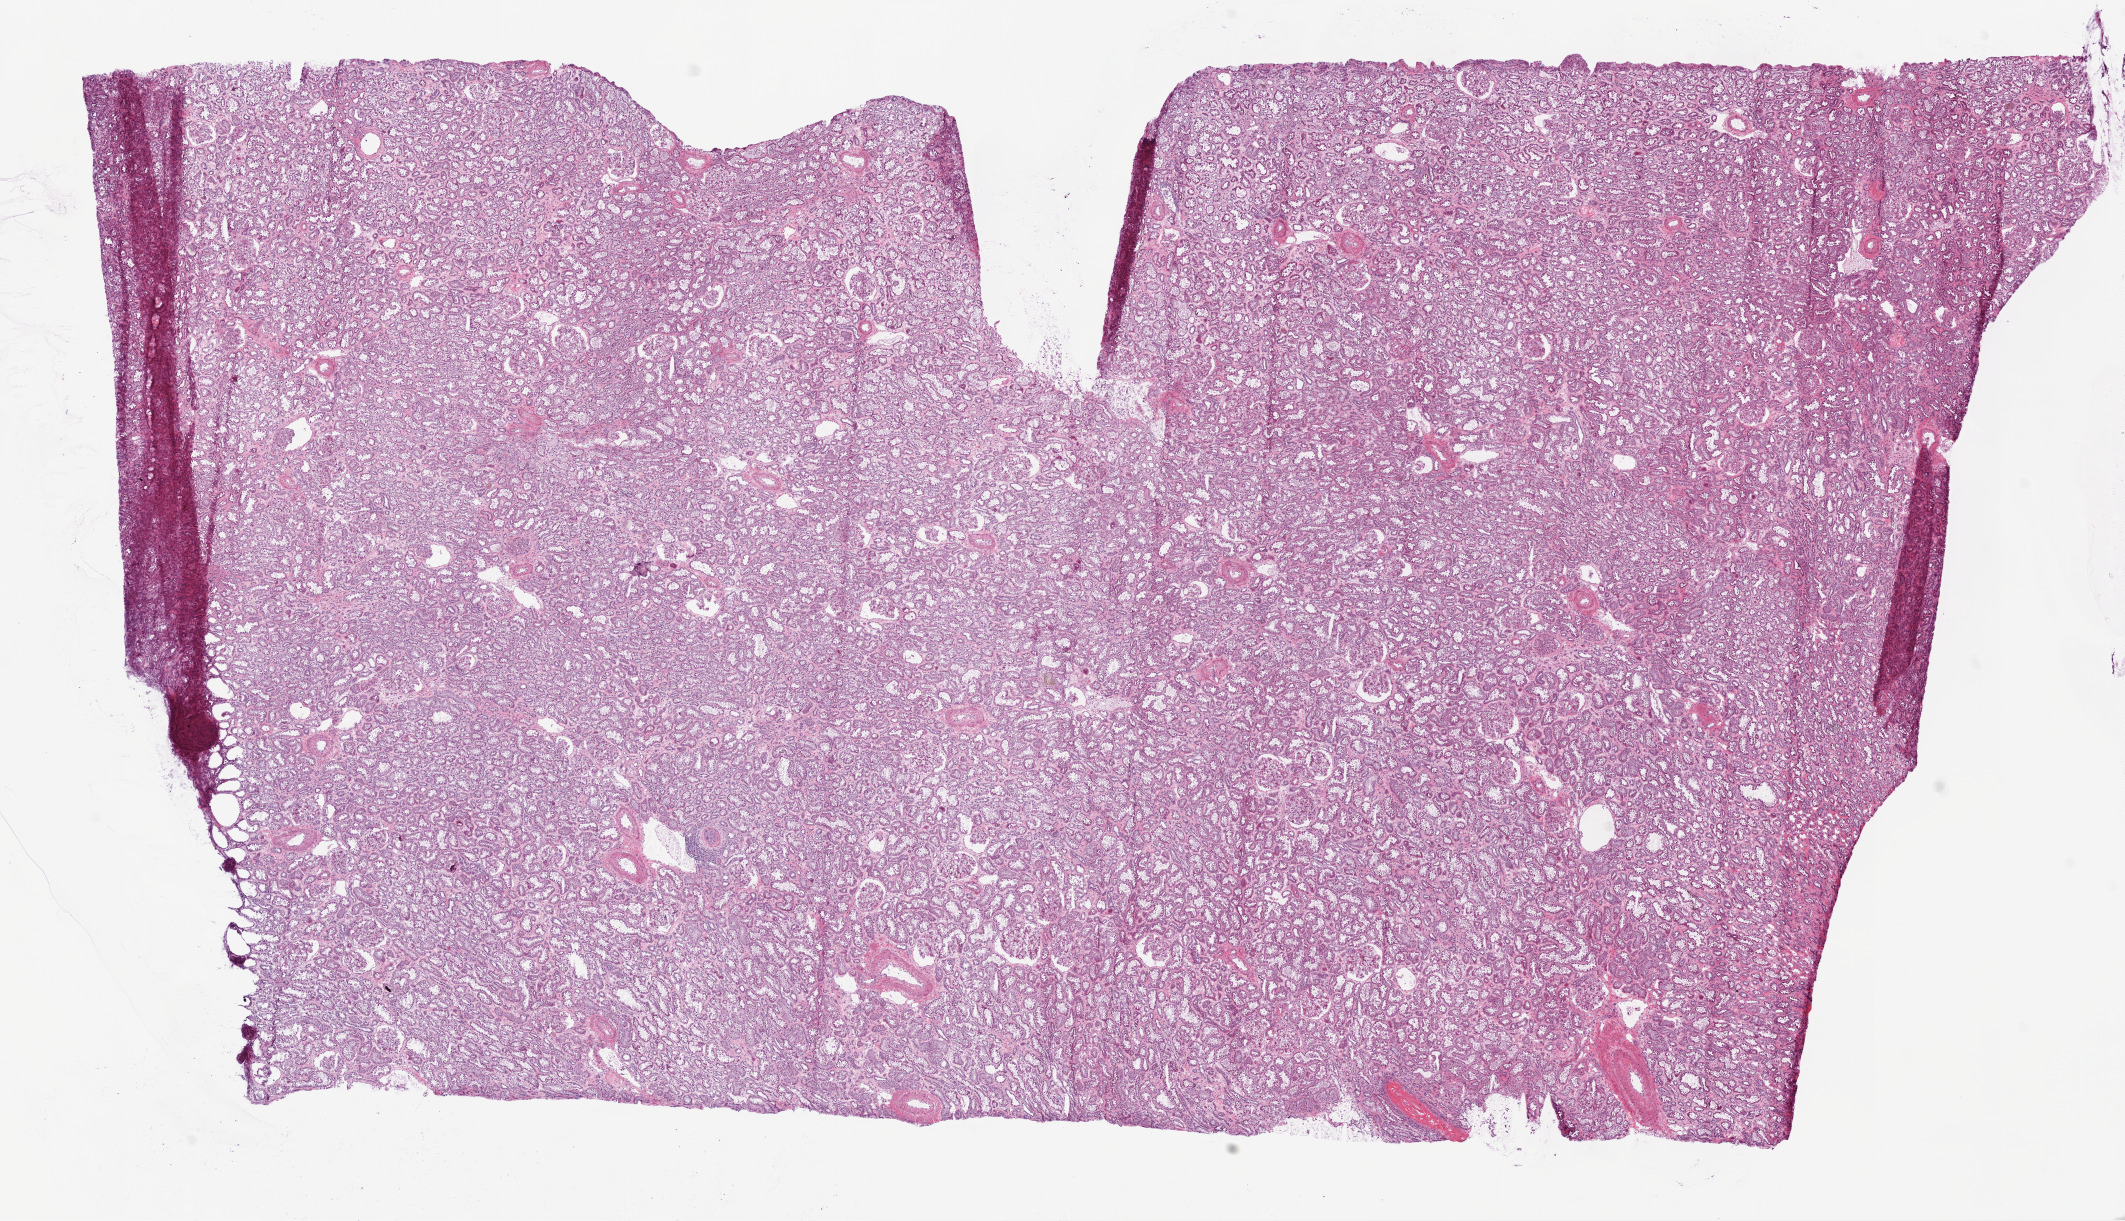
Hematoxylin and eosin (H&E) stained whole-slide image, shown as a low-resolution overview of the whole scanned area (about 17.1 x 9.8 mm, slide scanned at 20x). Frozen section. Kidney, solid tissue normal (non-tumour tissue) sample. Patient: male, age at initial diagnosis 52 years.
- this section: solid tissue normal sample (biorepository sample class)
- patient diagnosis: Clear cell adenocarcinoma, NOS